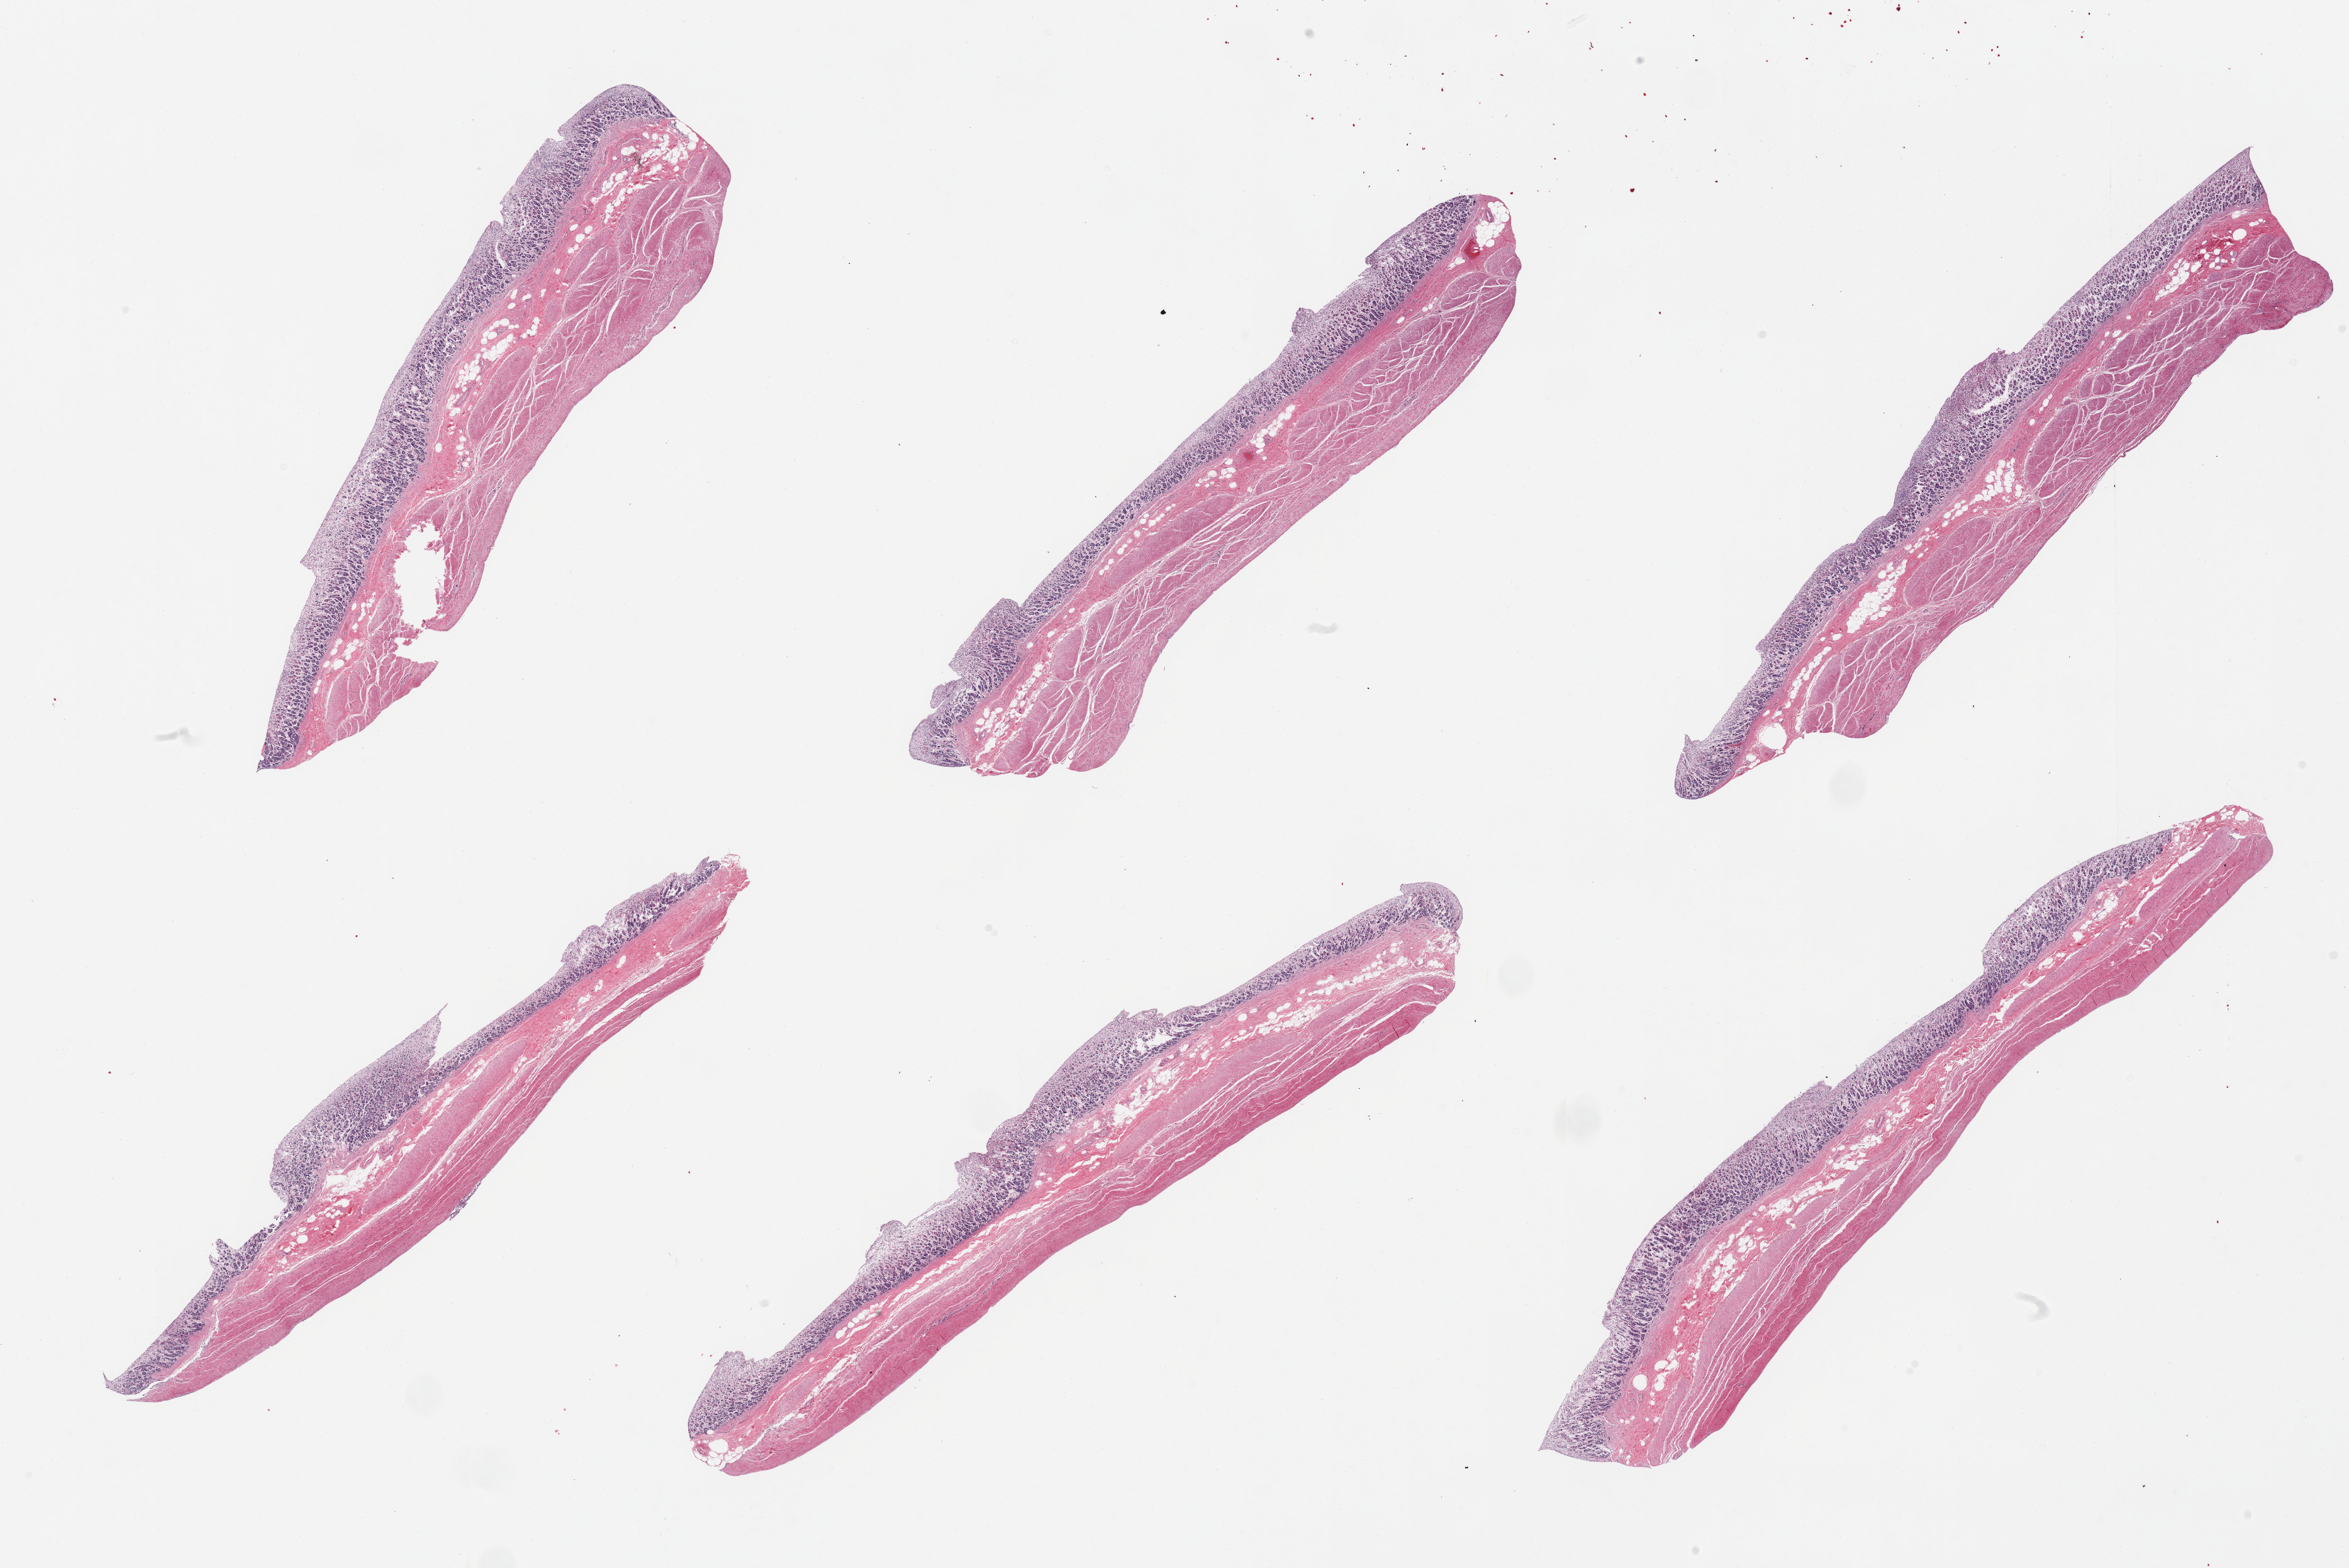
Whole-slide image, haematoxylin and eosin stain, brightfield, a low-resolution overview of the entire scanned area, about 29.5 x 19.7 mm (acquisition: 20x scan). PAXgene-fixed, paraffin-embedded tissue. Target tissue: stomach. Donor tissue sample. Donor: male.
Reviewer comment on this tissue sample: 6 pieces, mucosa up to ~0.5mm, ~30% thickness, but advance autolysis.